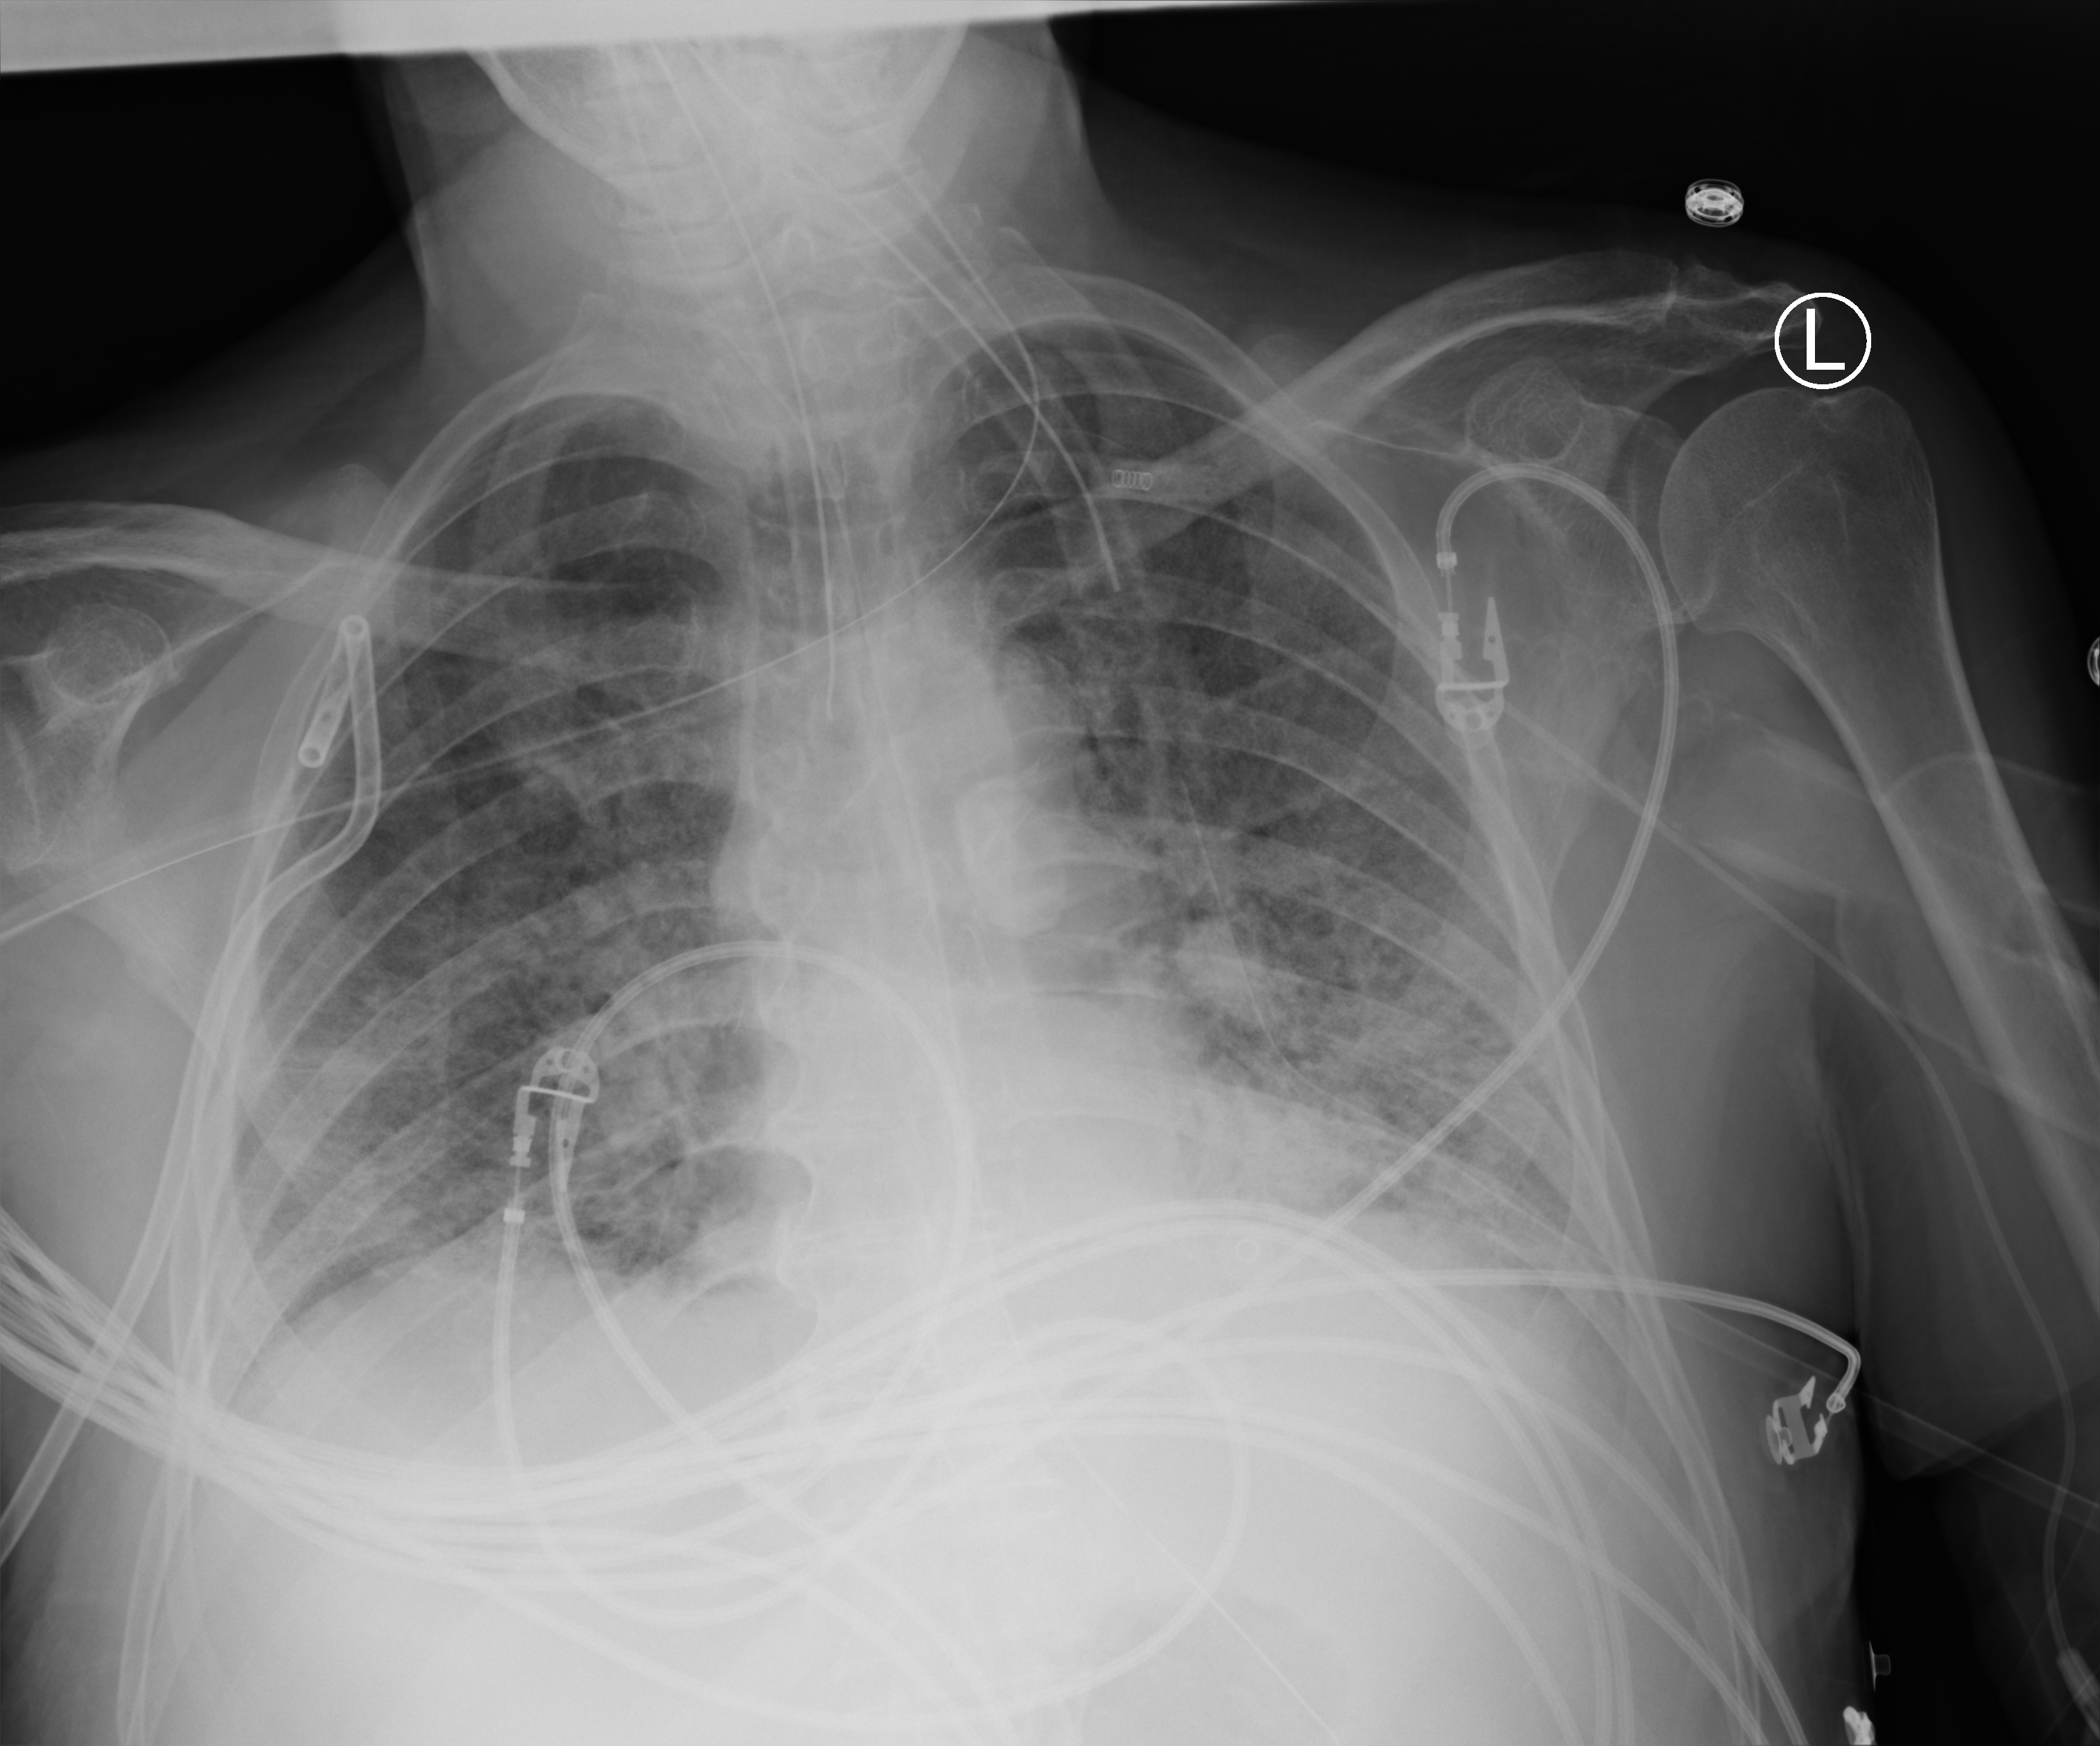
Bedside chest radiograph (computed radiography), anteroposterior (AP) projection. Male patient hospitalised with COVID-19, age 75–90 years.
Hospital-stay facts (about this admission, not read from this image; timing relative to this image not recorded): admitted to intensive care during this hospital stay: yes; mechanically ventilated during this hospital stay: yes.